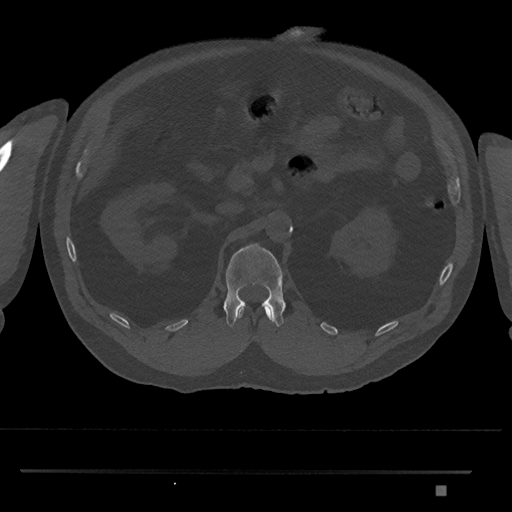
CT including the spine, one axial slice; slice 838 of 1134 in the series (ordered by position); reconstruction kernel Br40s/3; bone window (W 1800 / L 400 HU); 0.5 mm slice thickness; 512 × 512 image matrix, field of view 429 × 429 mm. Patient: male, 65 years. From the clinical record (not read from this slice): primary cancer: prostate.
Annotated regions visible in this slice (semi-automatically segmented with operator editing):
- L1 vertebra: bounding box (x1, y1, x2, y2) in pixels: (223, 243, 286, 327)
- T12 vertebra: (236, 308, 272, 319)